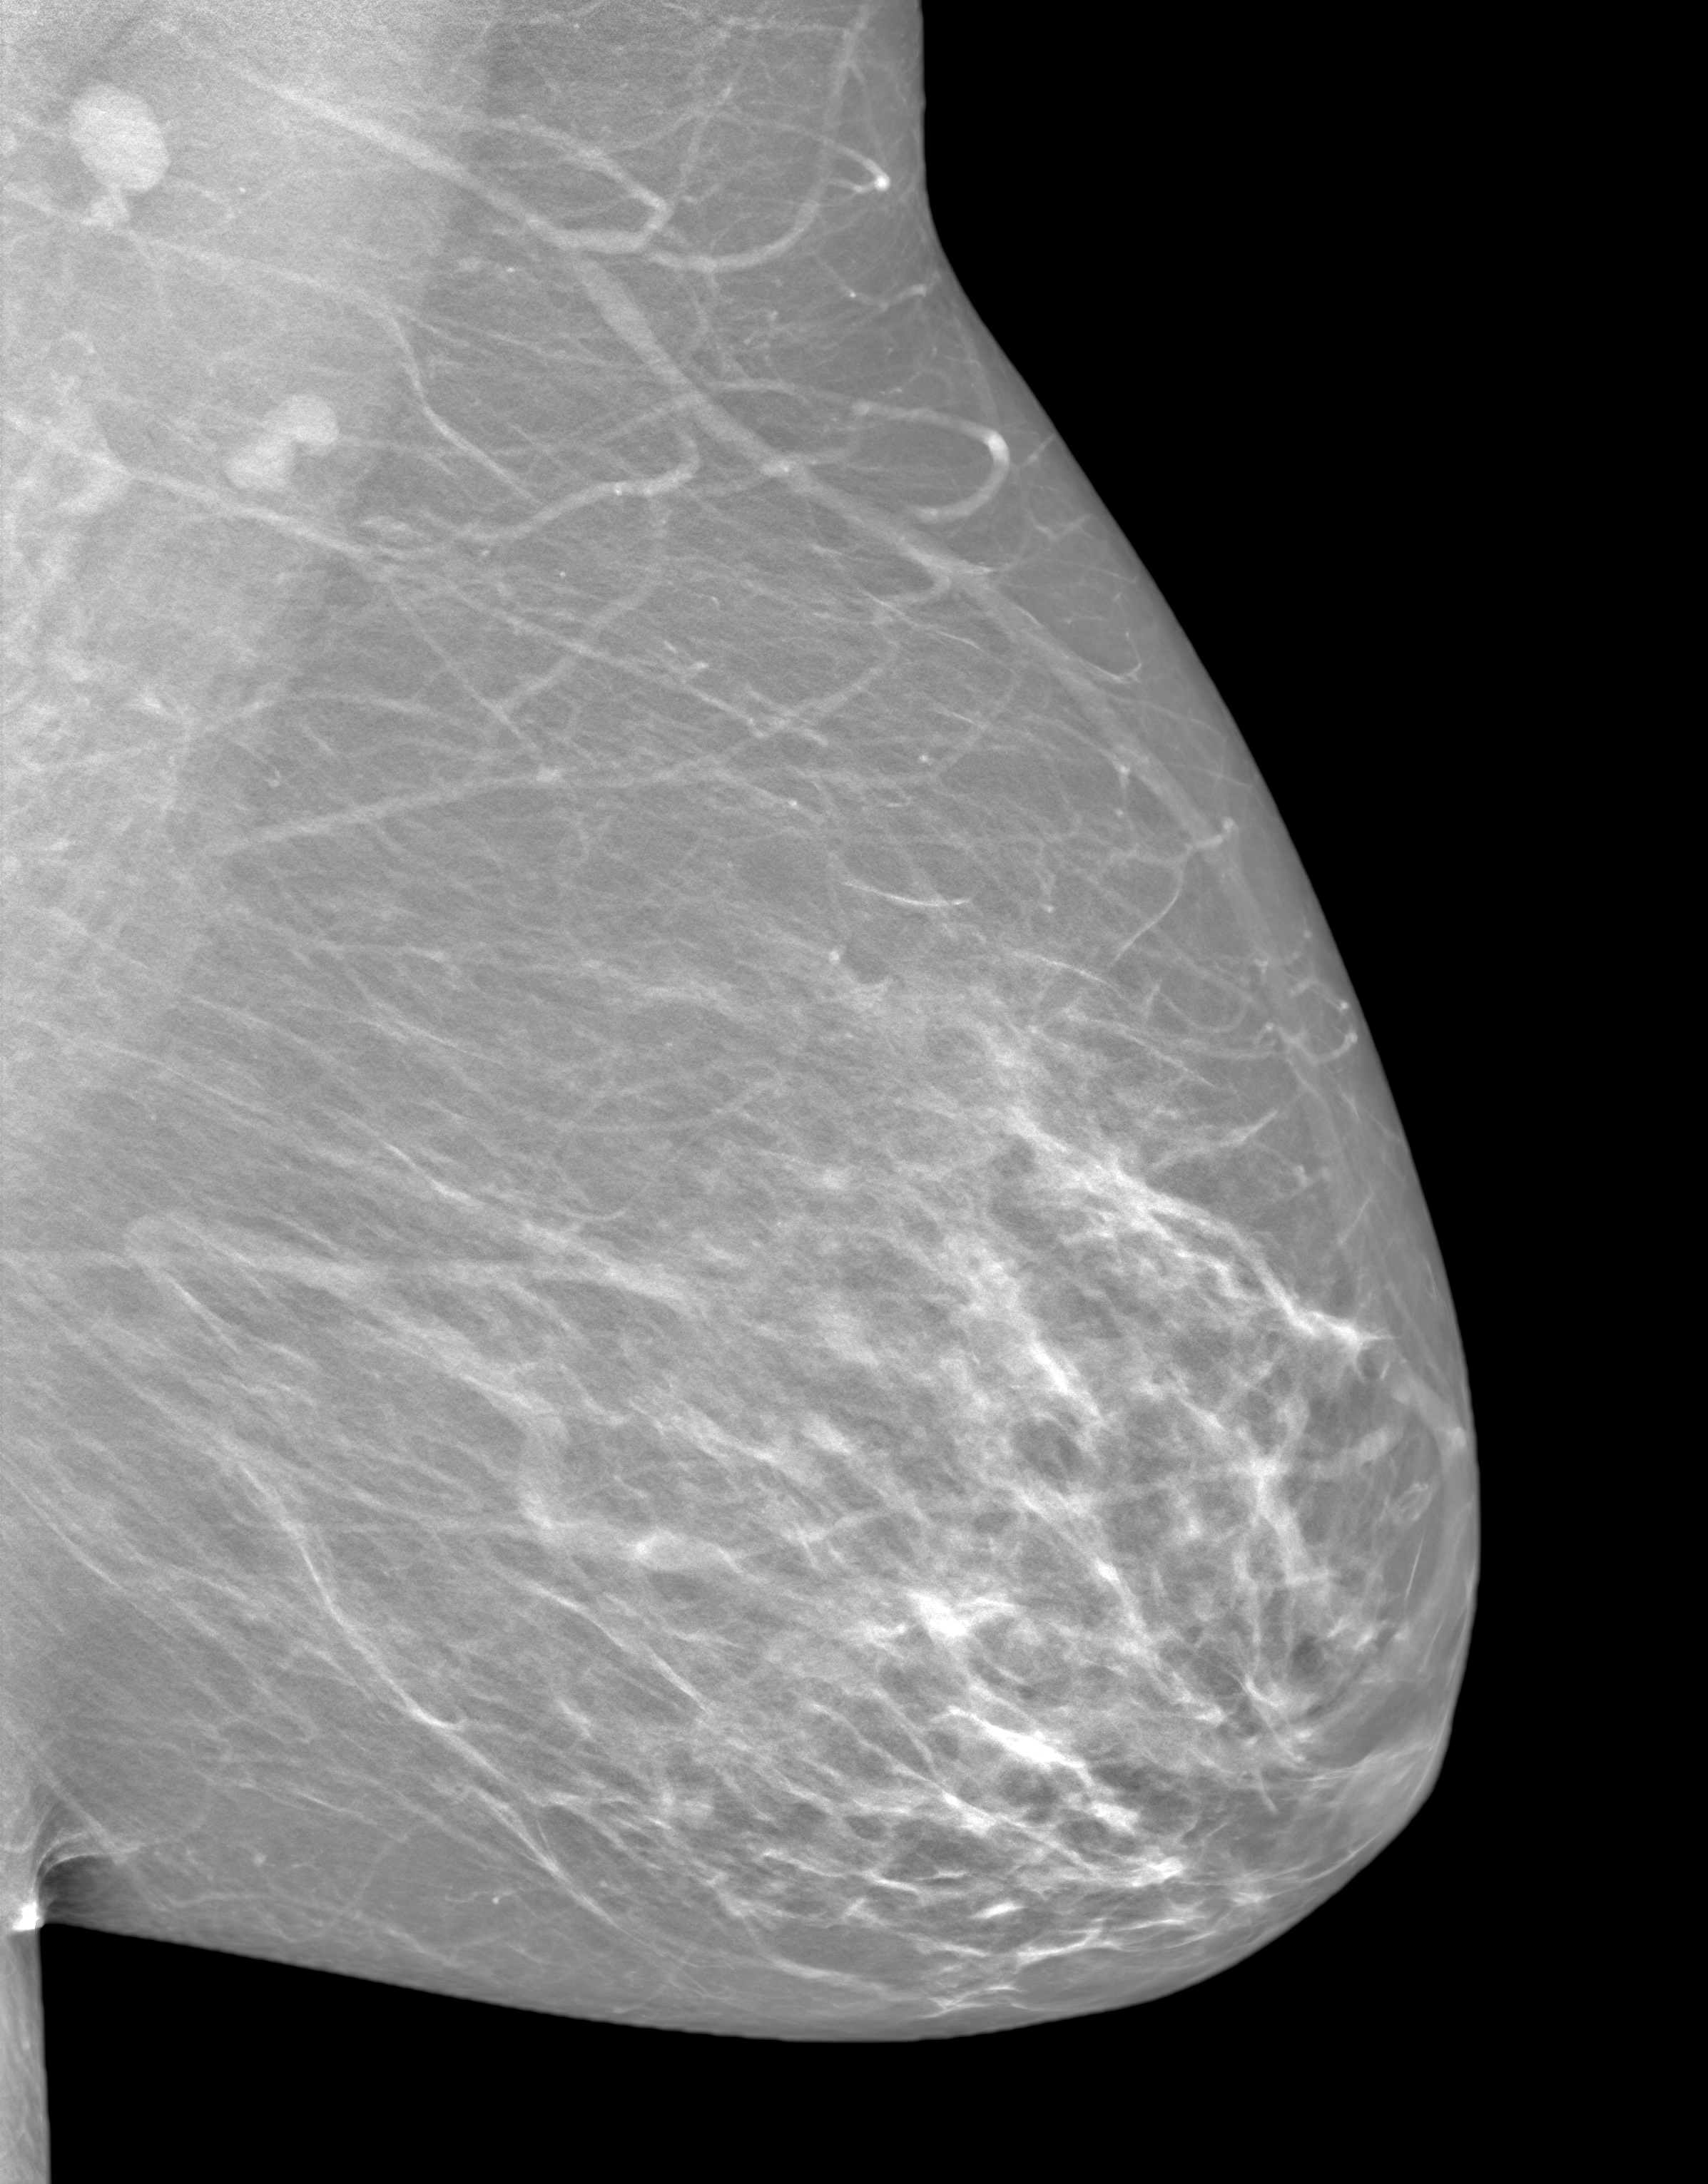
Annual screening mammography examination. Patient aged 59 years (female).
Image type: synthesized 2-D view from tomosynthesis. Breast: left. Projection: medio-lateral oblique projection.